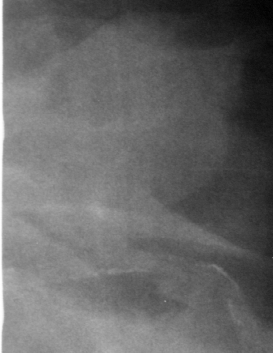
Crop from a digitized film mammogram around one marked abnormality, left breast, CC view, BI-RADS breast density category 4 (scale 1–4).
Finding: mass, shape lobulated, margins circumscribed; BI-RADS assessment category 3; pathology (as recorded): benign.